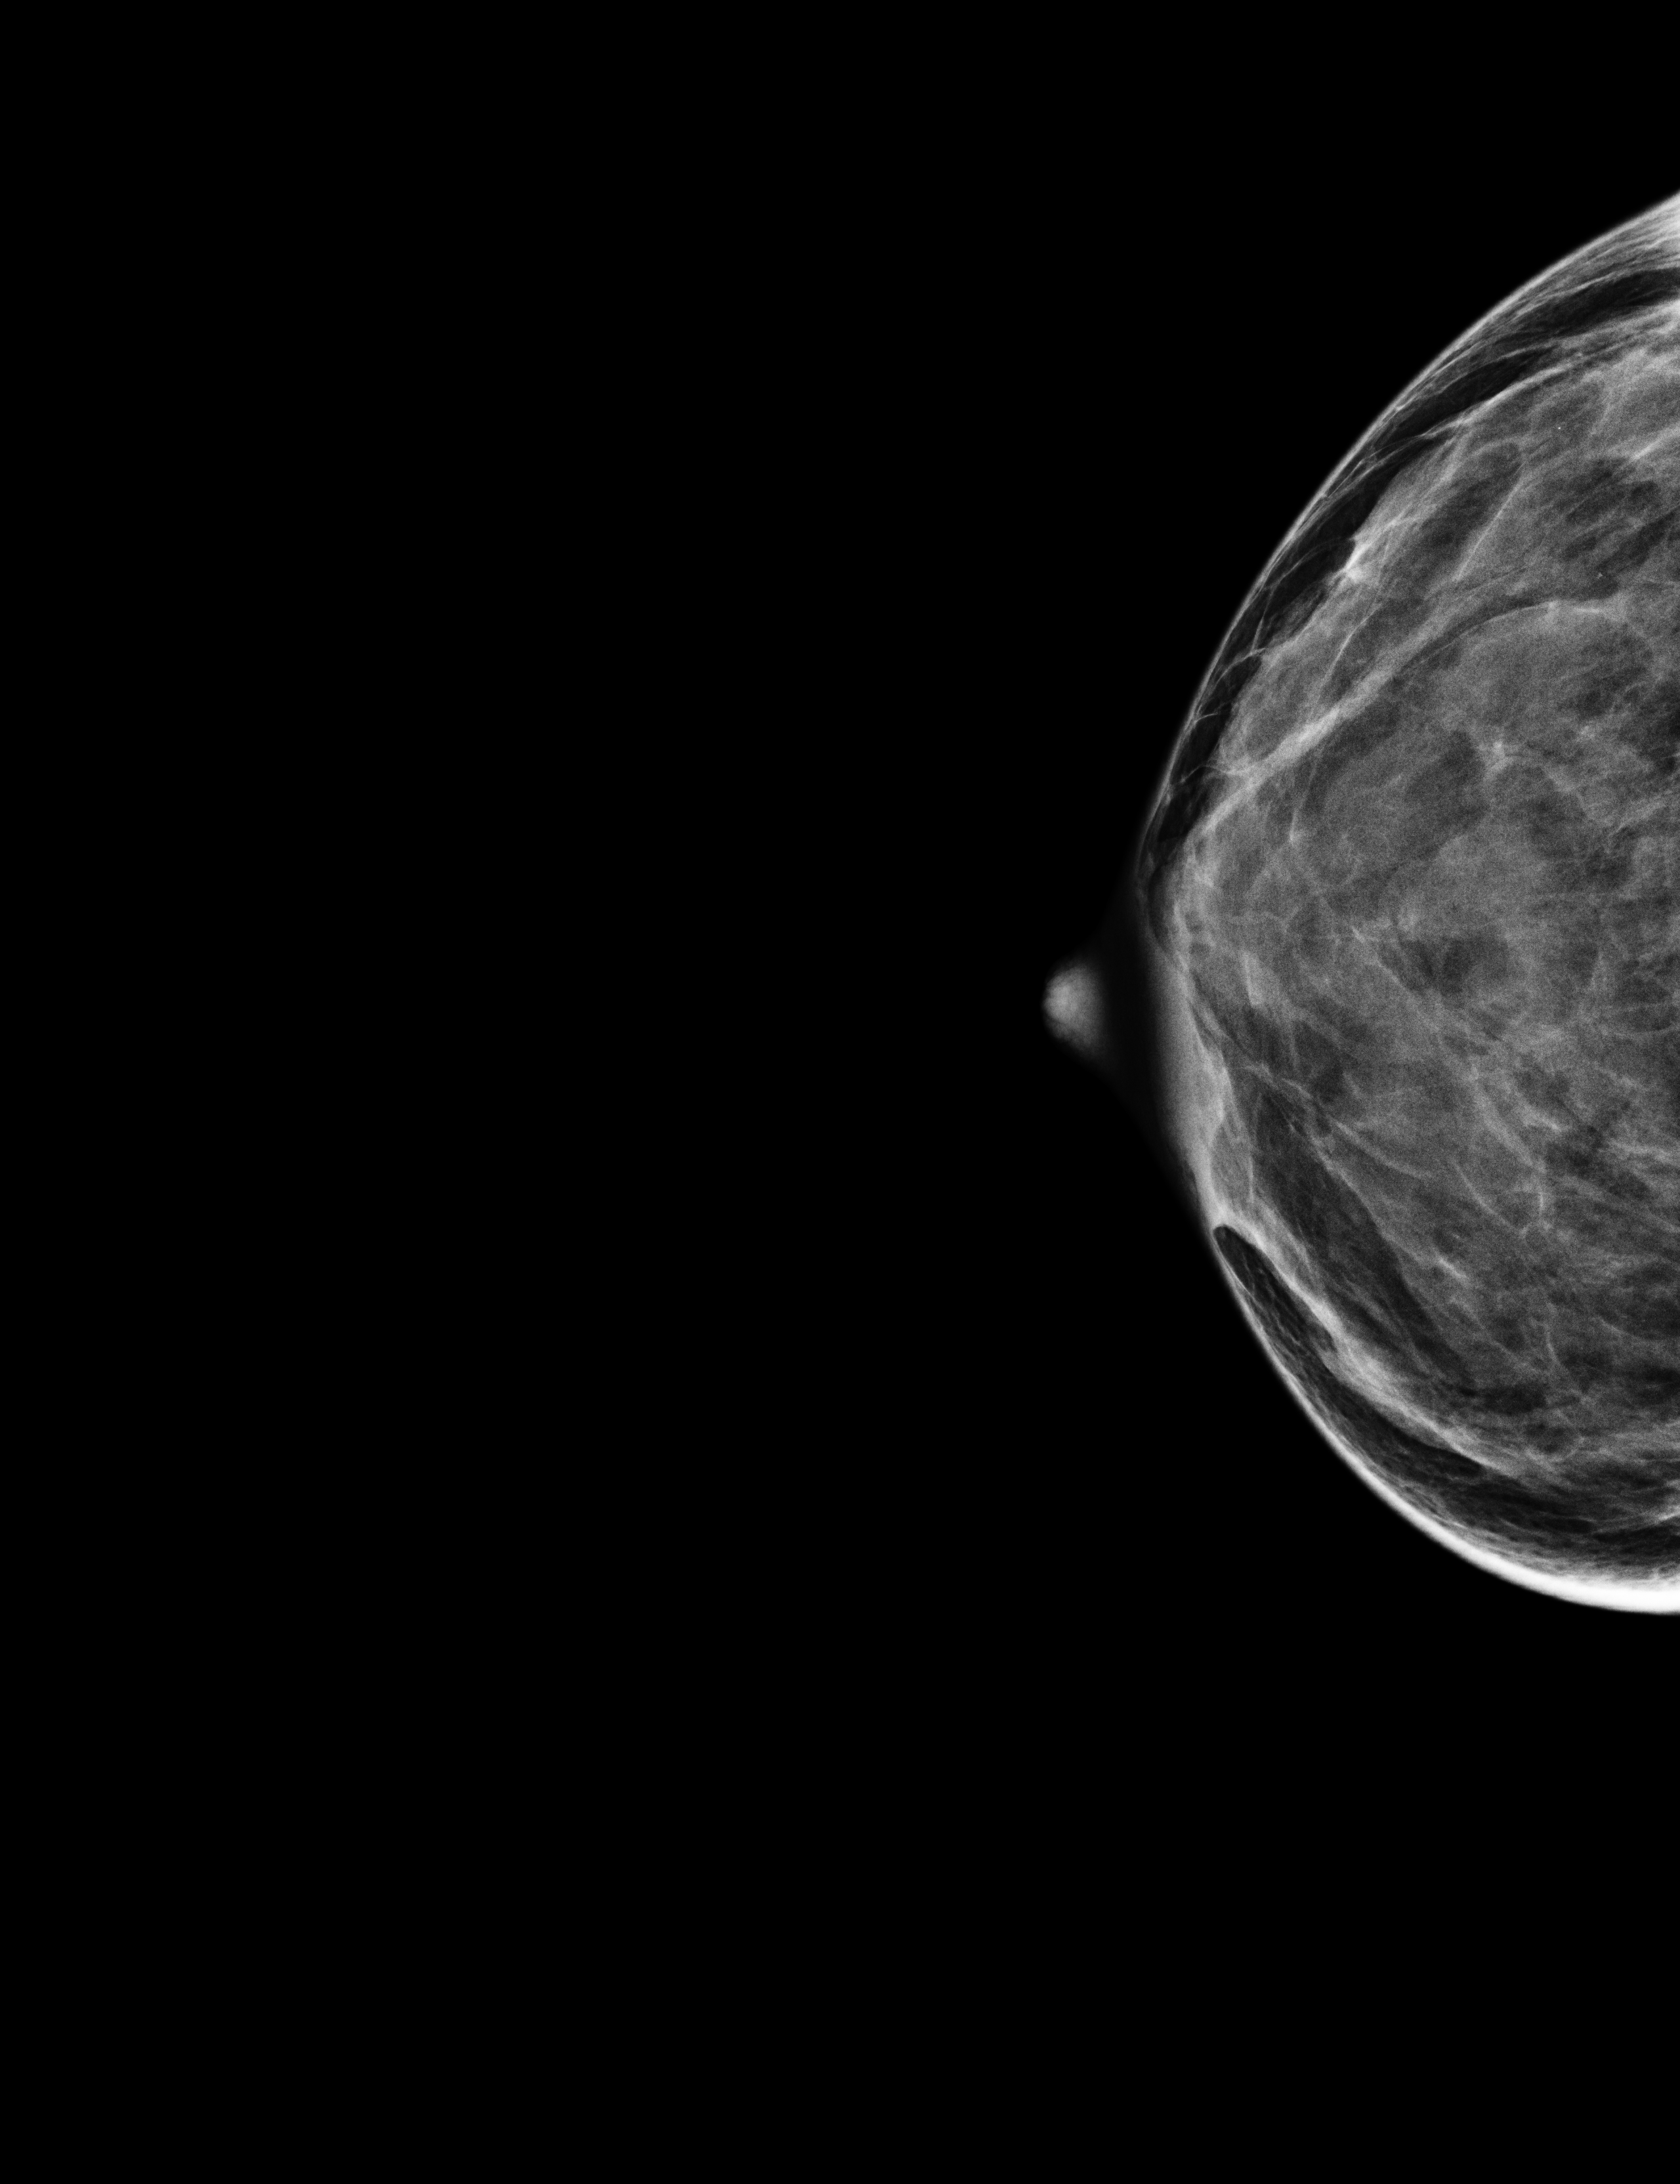
Full-field digital mammogram (FFDM); right breast; craniocaudal (CC) view; annual screening mammography examination; compressed breast thickness 38 mm. Female patient, age 42 years.
- BI-RADS breast density category at the screening exam (both breasts, scale 1–4): 4
- final BI-RADS assessment for this screening round (tomosynthesis exam, both breasts): category 1
- recall: no recall after this screen